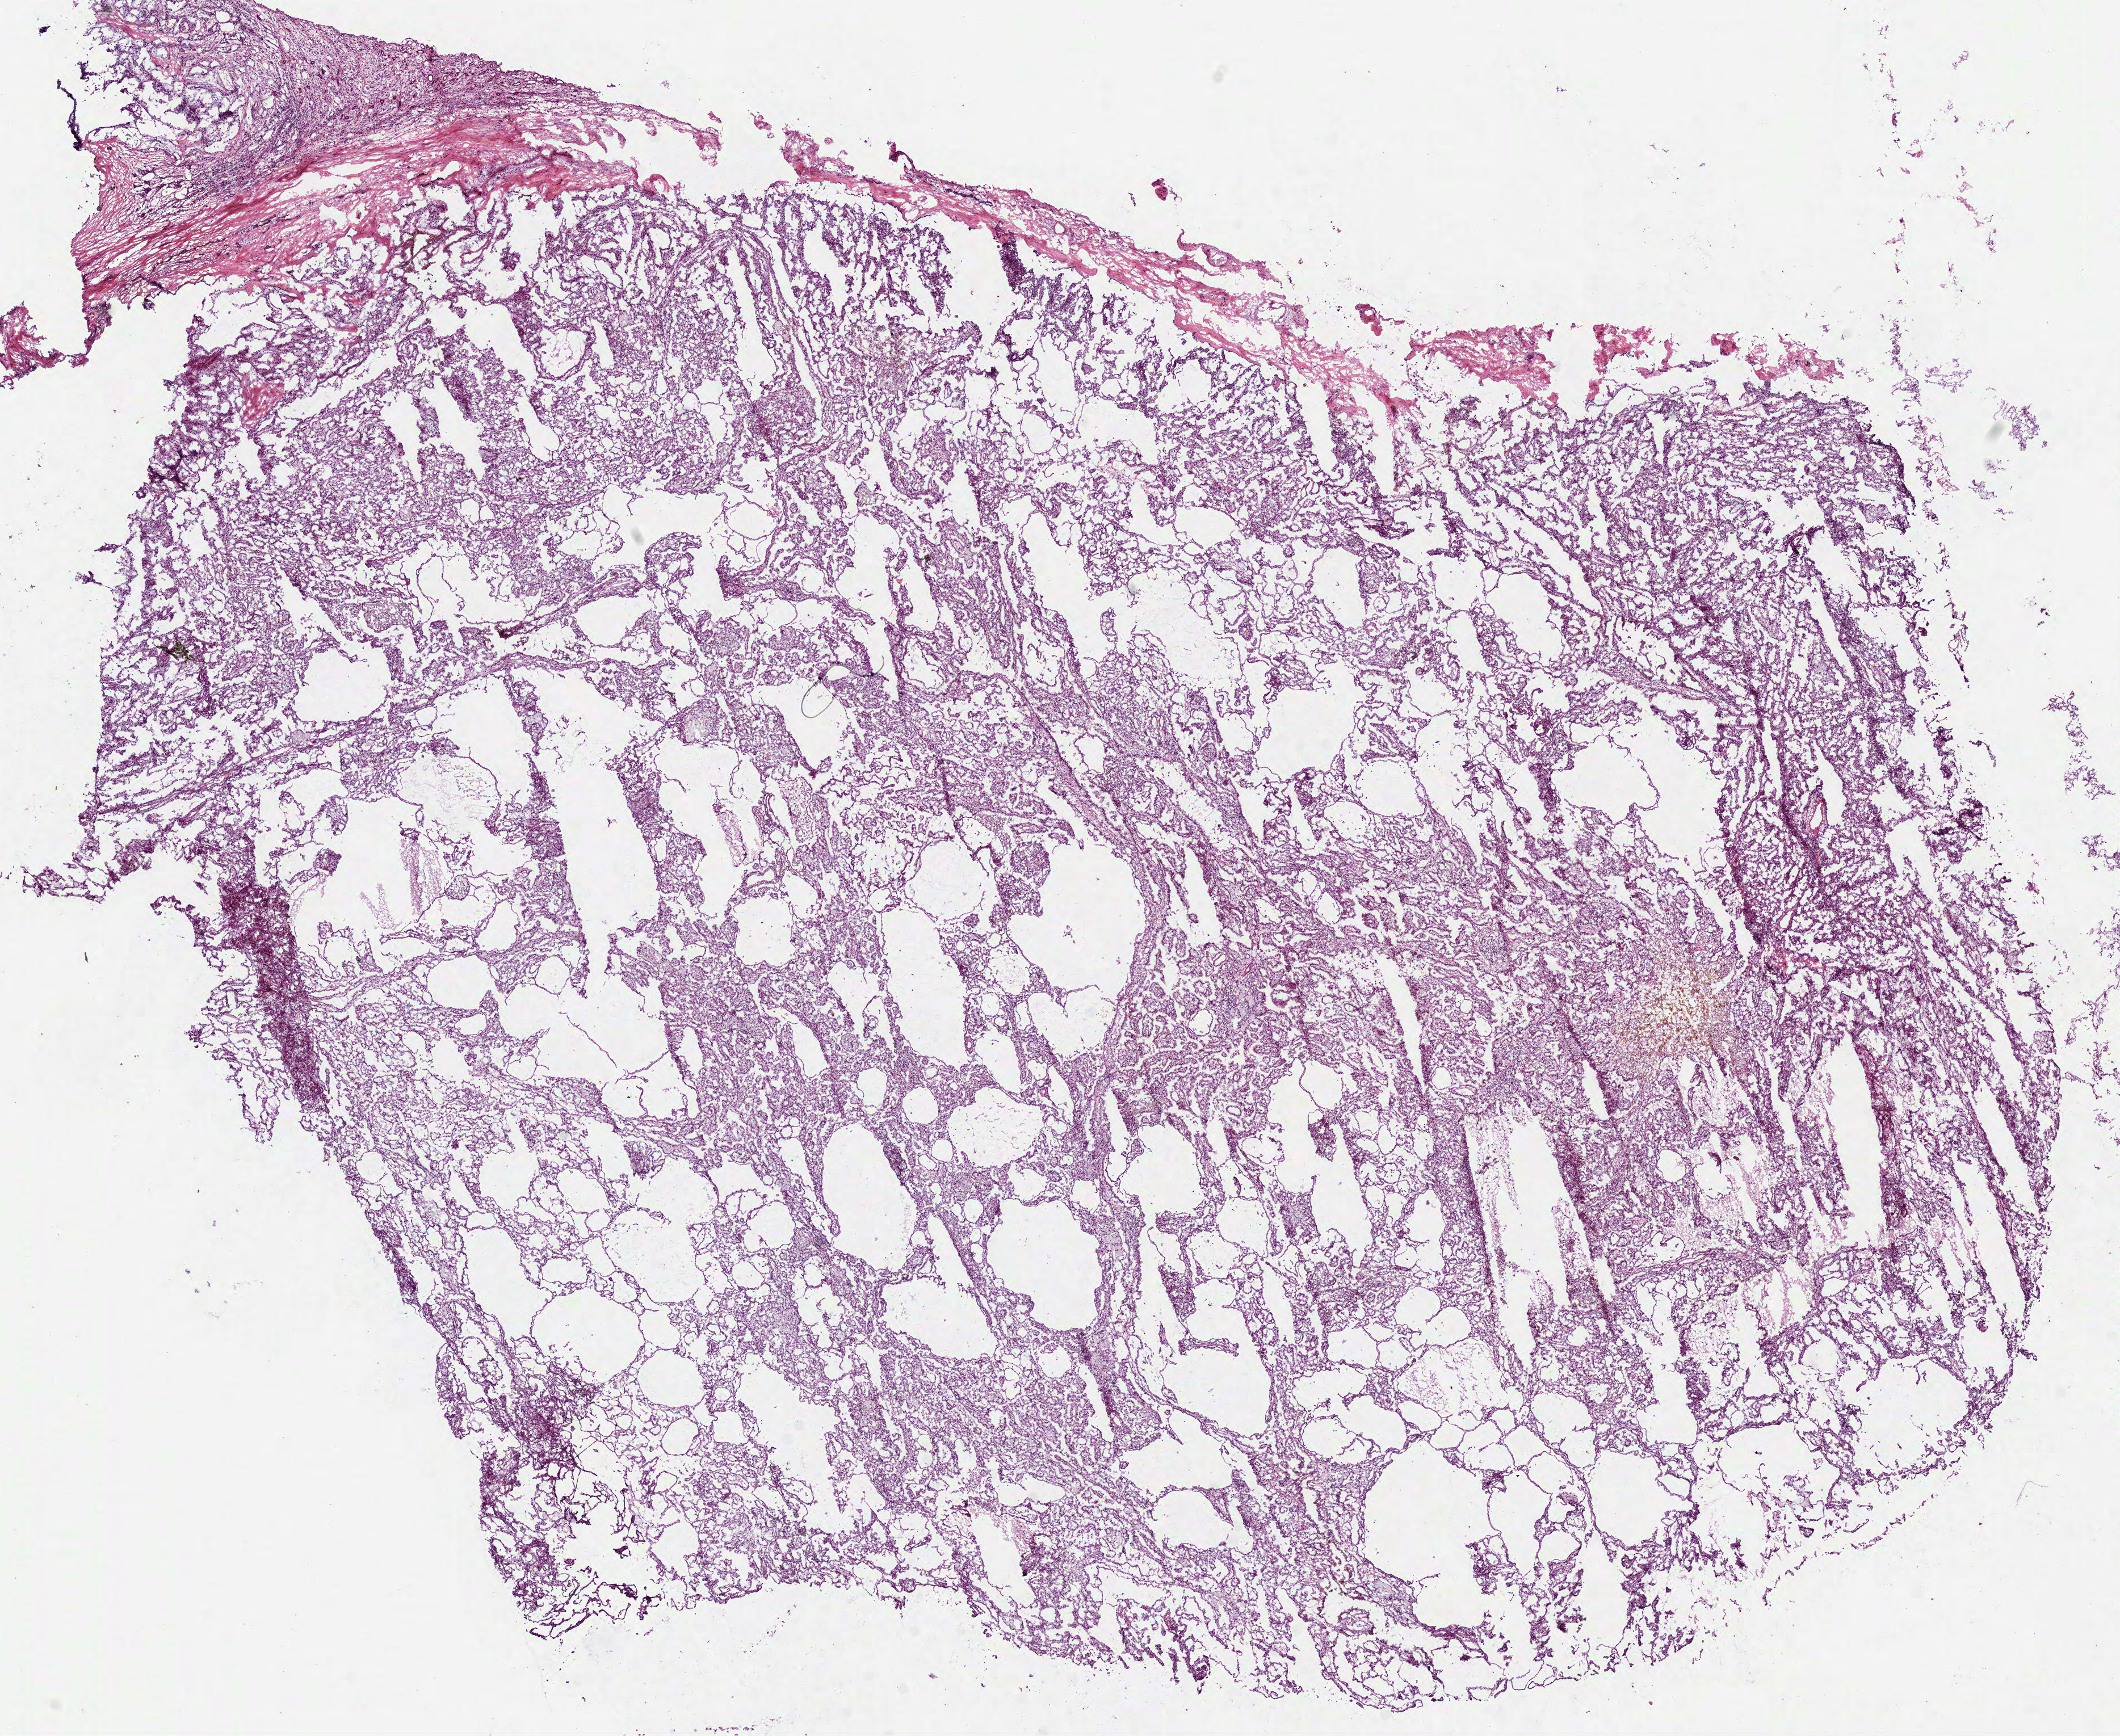
Whole-slide histology image, H&E-stained — shown as a low-resolution overview of the whole scanned area (about 15.1 x 12.3 mm); frozen section; primary tumour sample from the kidney. Male, age 42 years at initial diagnosis. Pathologist review of this section (percent, as recorded): tumour cells 80%, tumour nuclei 75%, normal cells 5%, stromal cells 15%, necrosis 0%.
- TNM: T1 N0 M0
- AJCC pathologic stage: I (6th edition)
- pathologic diagnosis: Papillary adenocarcinoma, NOS